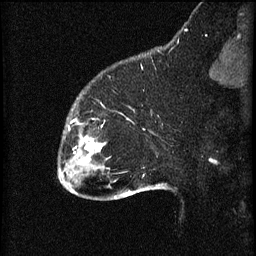
Breast MRI (dynamic contrast-enhanced), one sagittal slice. Slice 14 of 60 in the series (ordered by position). 3 images stored at this slice position (order not interpretable as contrast timing). 1.5 T. TE 4.2 ms, TR 8.2 ms. 2 mm slice thickness. 256 × 256 image matrix, field of view 180 × 180 mm. Female patient, age 32 years.
Annotated regions visible in this slice (semi-automatic segmentation, software-assisted and operator-edited):
- analysis volume of interest (the breast-tissue region the enhancement analysis was run in; not a lesion): bounding box <59,106,111,165> (left, top, right, bottom; pixels)
- tumour enhancement mask (voxels above the 70 % enhancement threshold inside the analysis volume of interest): <68,126,101,163>